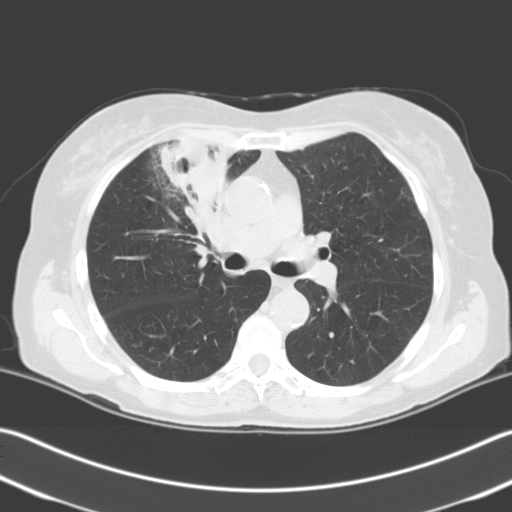
Low-dose screening chest CT, one axial slice; slice 133 of 204 in the series (ordered by position); 140 kVp; lung window (W 1500 / L -600 HU); 3.2 mm slice thickness; 512 × 512 image matrix, field of view 348 × 348 mm.
Structures marked on this image (outlined manually by an expert reader):
- lesion 1 (tumor, upper lobe of right lung): box from (x=159, y=137) to (x=233, y=211) px